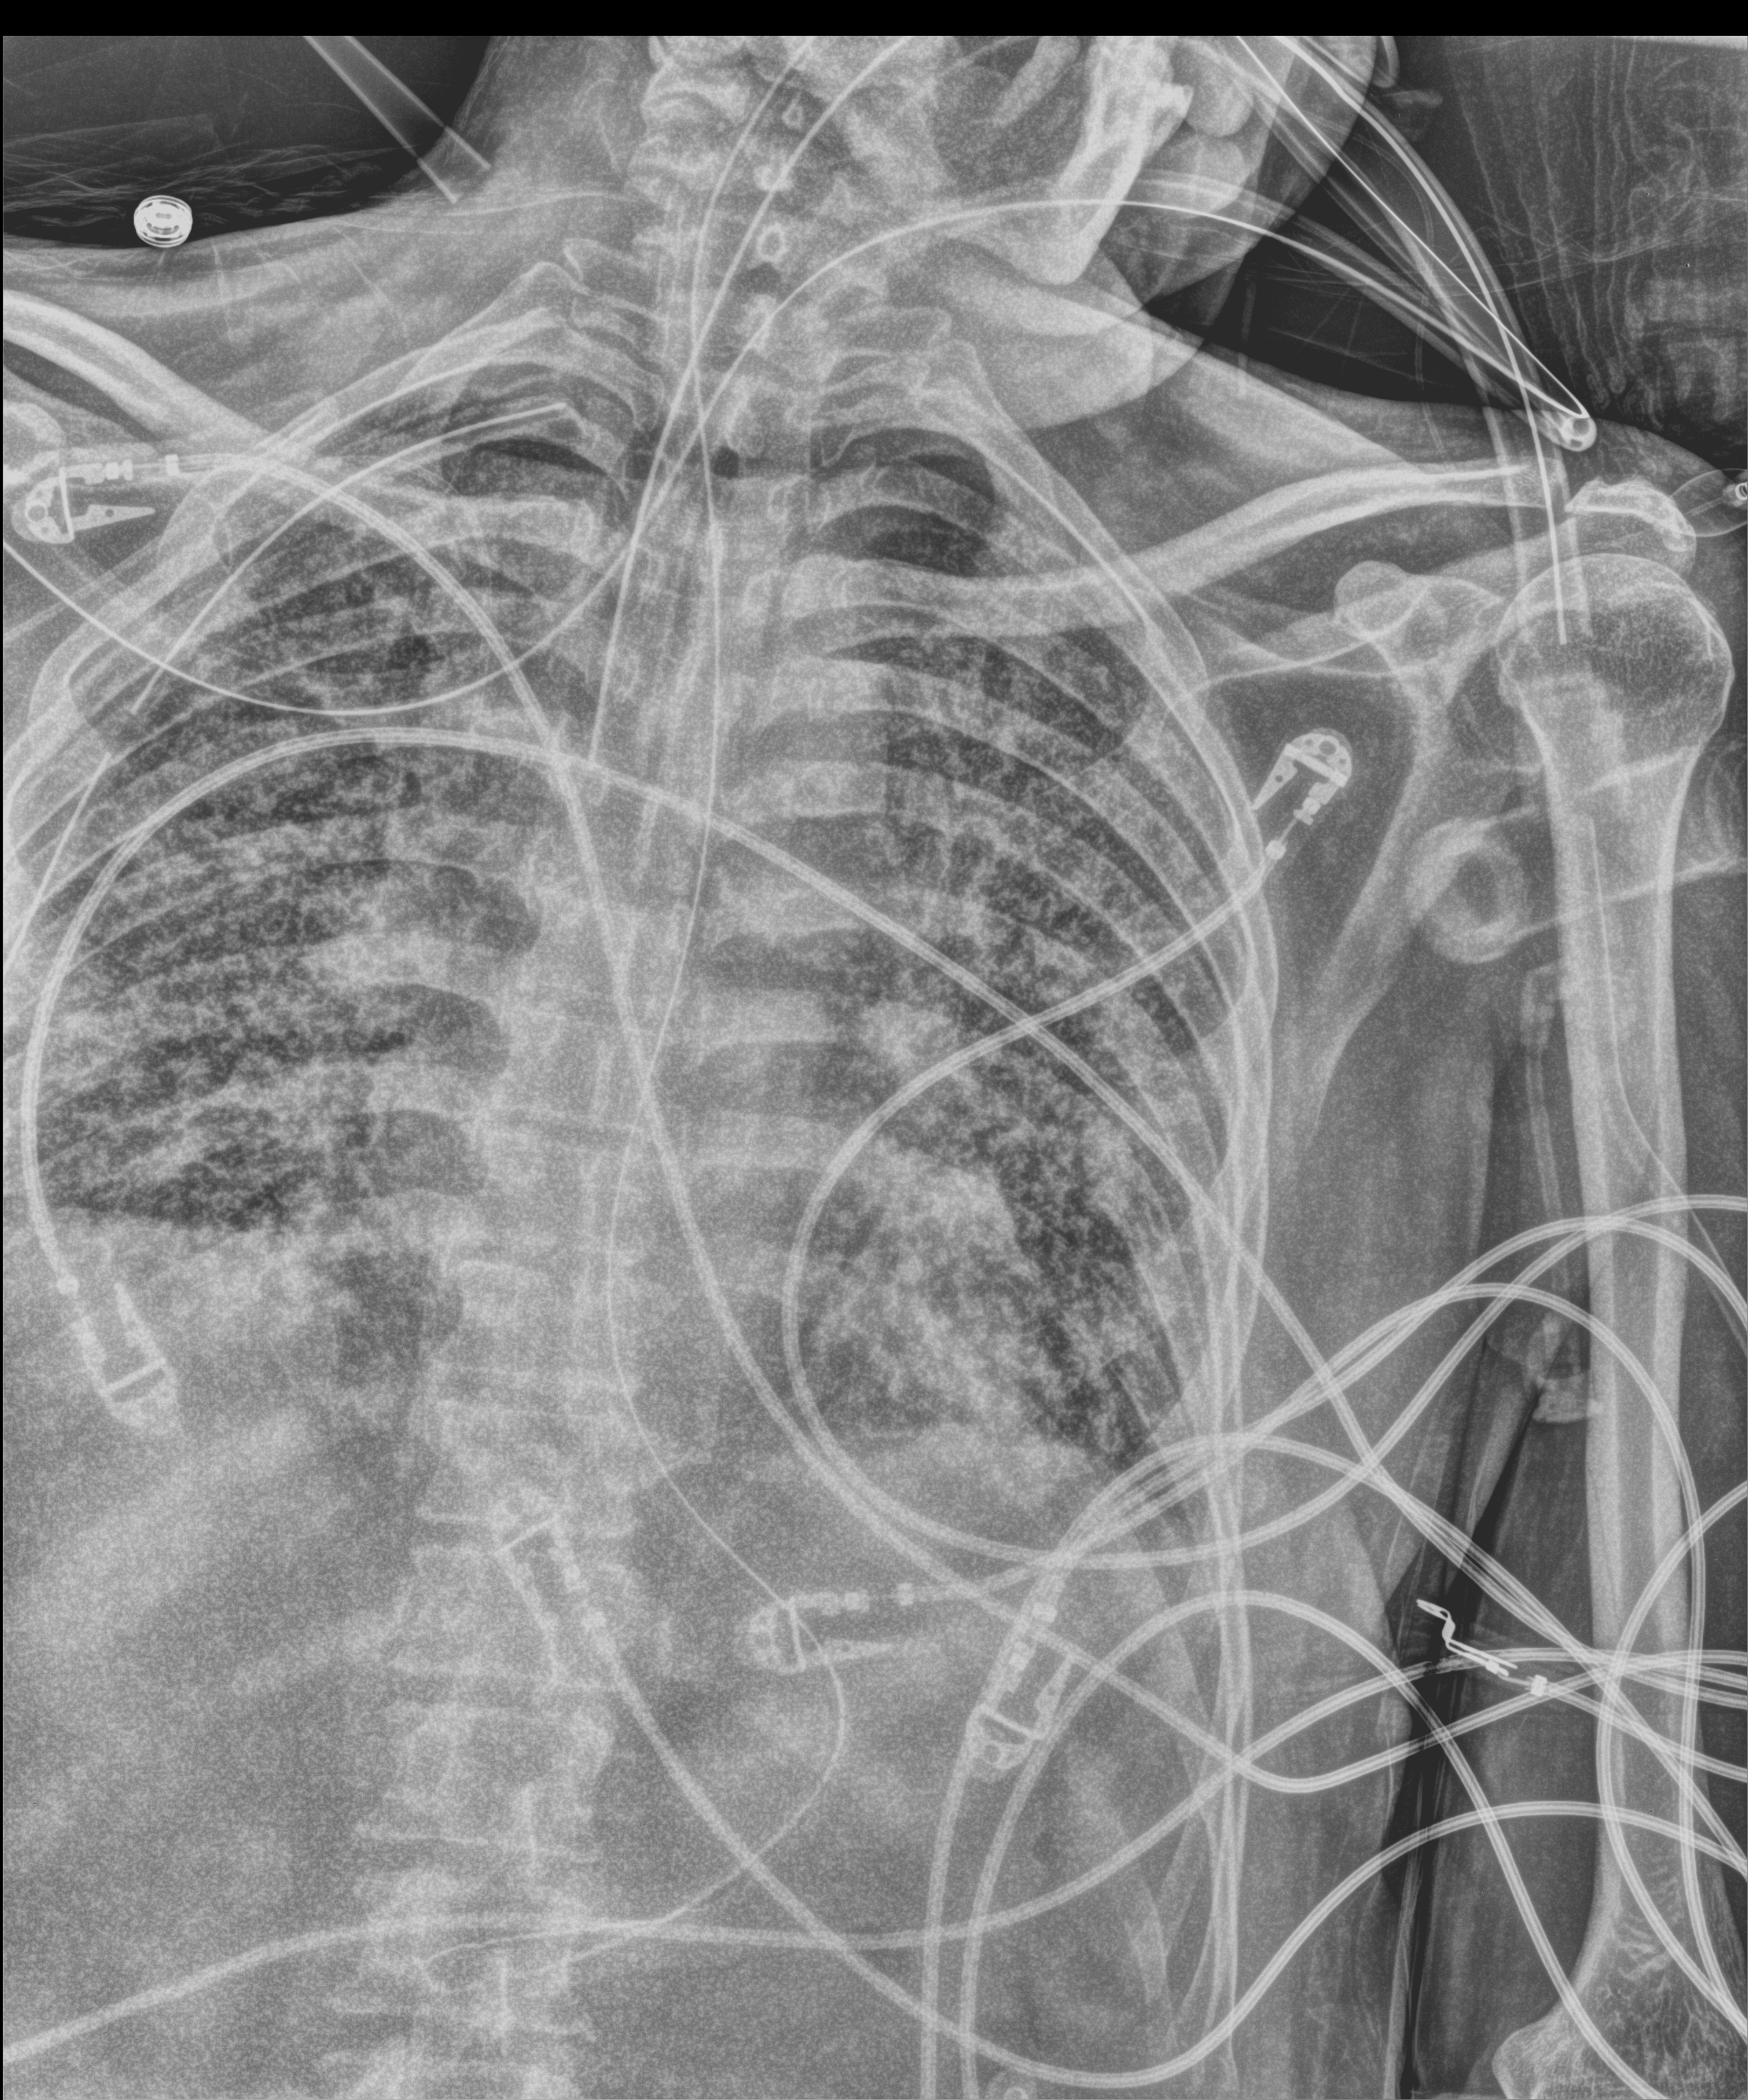
Chest X-ray (portable); anteroposterior (AP) projection. Patient hospitalised with COVID-19; male, aged 60–74 years.
Admission-level facts for this patient (not findings on this image; timing relative to this image not recorded): admitted to intensive care during this hospital stay: yes.